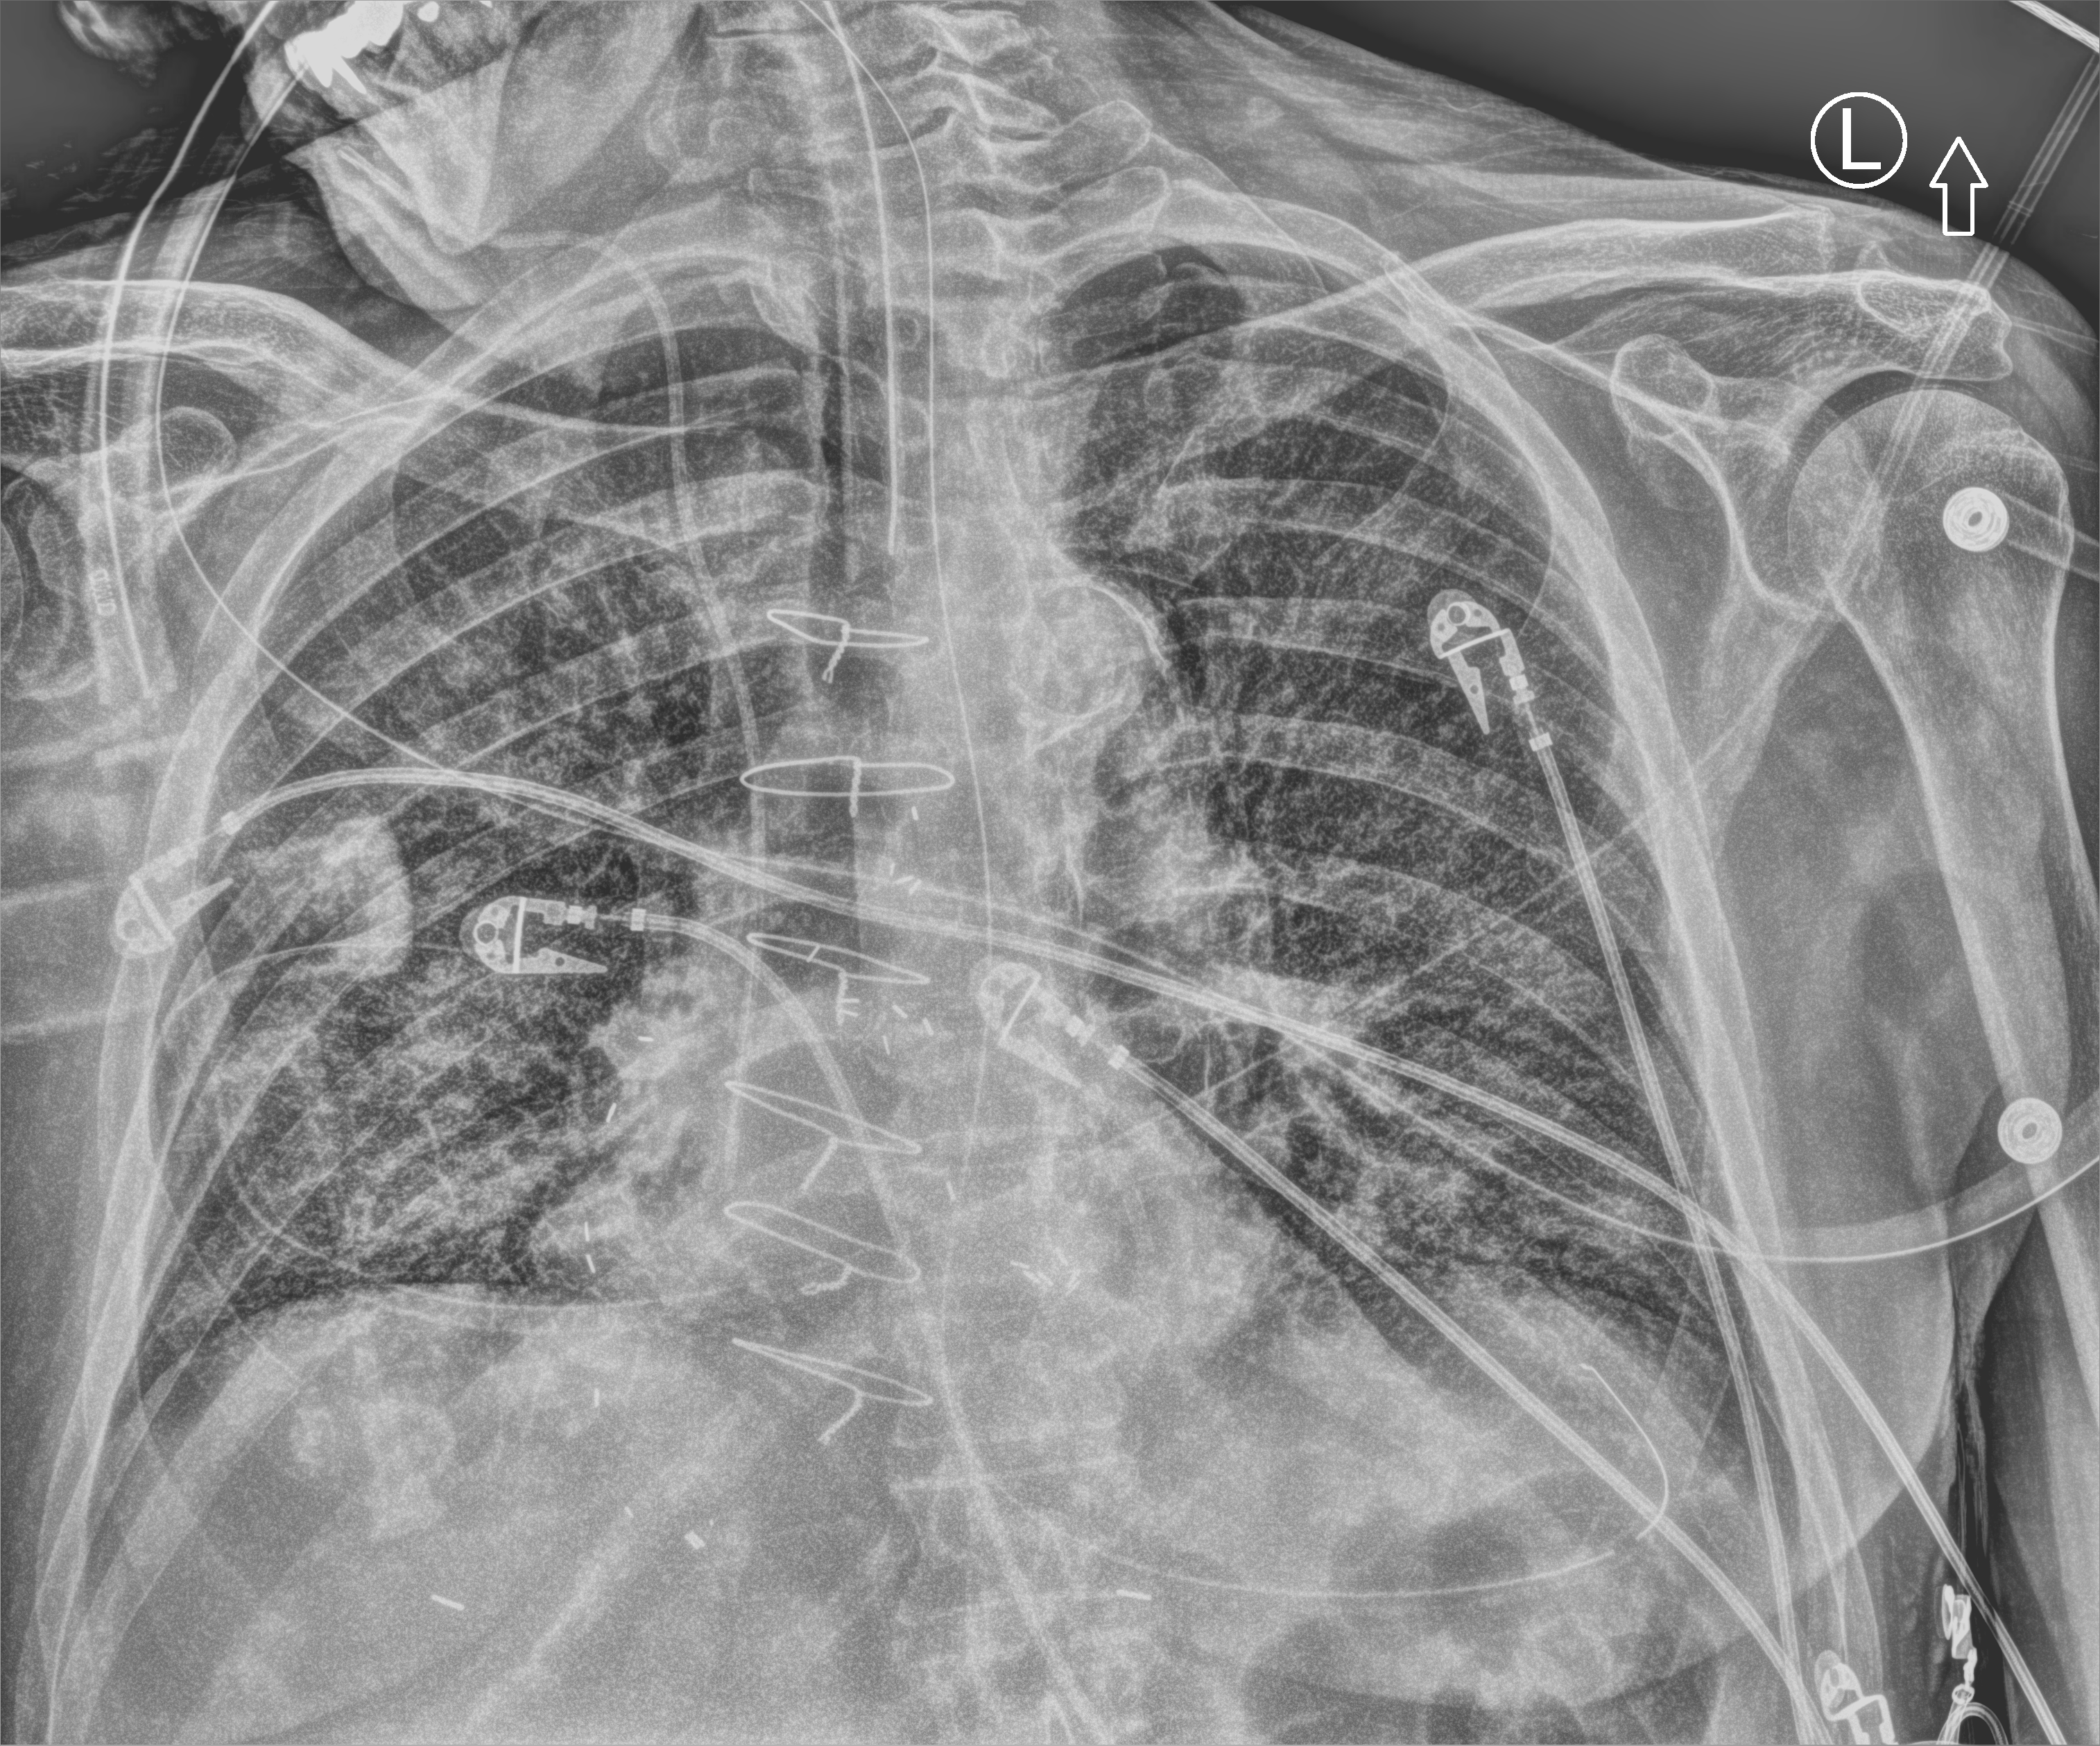
Chest X-ray (portable), anteroposterior (AP) projection. Male patient hospitalised with COVID-19, age 75–90 years.
Admission-level facts for this patient (not findings on this image; timing relative to this image not recorded): admitted to intensive care during this hospital stay: yes; other chronic lung disease (admission record): no; mechanically ventilated during this hospital stay: yes.